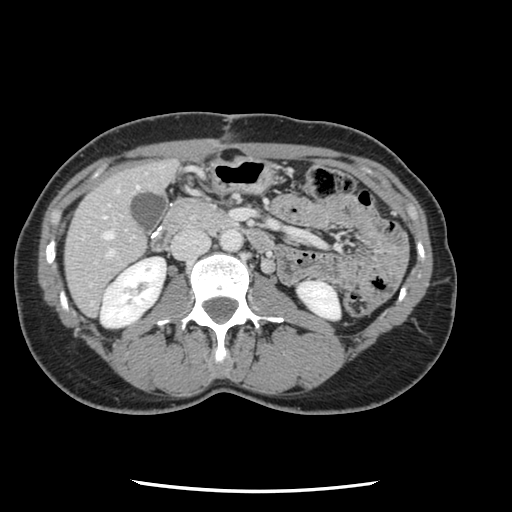
Contrast-enhanced abdominal CT, one axial slice; position 34 of 134 along the scan axis; 120 kVp; intravenous contrast given; soft-tissue window (W 400 / L 40 HU); 2.5 mm slice thickness; 512 × 512 image matrix, field of view 330 × 330 mm. Female patient, age 43 years. From the clinical record (not read from this slice): diagnosis: colorectal cancer liver metastases, imaged before liver resection; multiple liver metastases: yes; largest metastasis: 3.4 cm; disease in both lobes: yes.
Outlined on this slice (expert manual segmentation):
- hepatic veins: bounding box (x1, y1, x2, y2) in pixels: (104, 187, 138, 239)
- liver: (66, 161, 176, 315)
- planned liver remnant (the part of the liver to remain after resection): (66, 161, 177, 315)